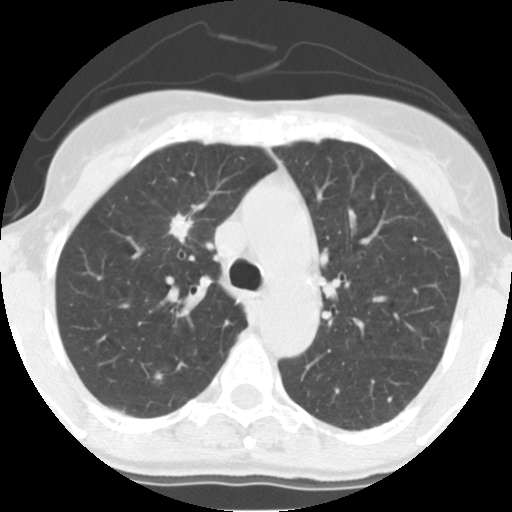
Axial slice from a low-dose chest CT screening exam; third screening round (two years after baseline); lung window (W 1500 / L -600 HU); 2.5 mm slice thickness; slice 44 of 140 in the series. Female, age 56 years at enrolment.
Lesion marked by an expert reader, box from (x=161, y=210) to (x=199, y=248) px. Screening reader's record for this exam (one nodule recorded; not confirmed to be the boxed lesion): non-calcified nodule or mass ≥4 mm, right upper lobe, 17 × 12 mm, spiculated (stellate) margins, soft tissue attenuation, pre-existing on the prior screen: yes; interval growth: yes. Official screen result: positive, other. Lung cancer was diagnosed 49 days after this screen: adenocarcinoma, NOS, right upper lobe, moderately differentiated (G2), stage IA (AJCC 6th edition), 19 mm at pathology.